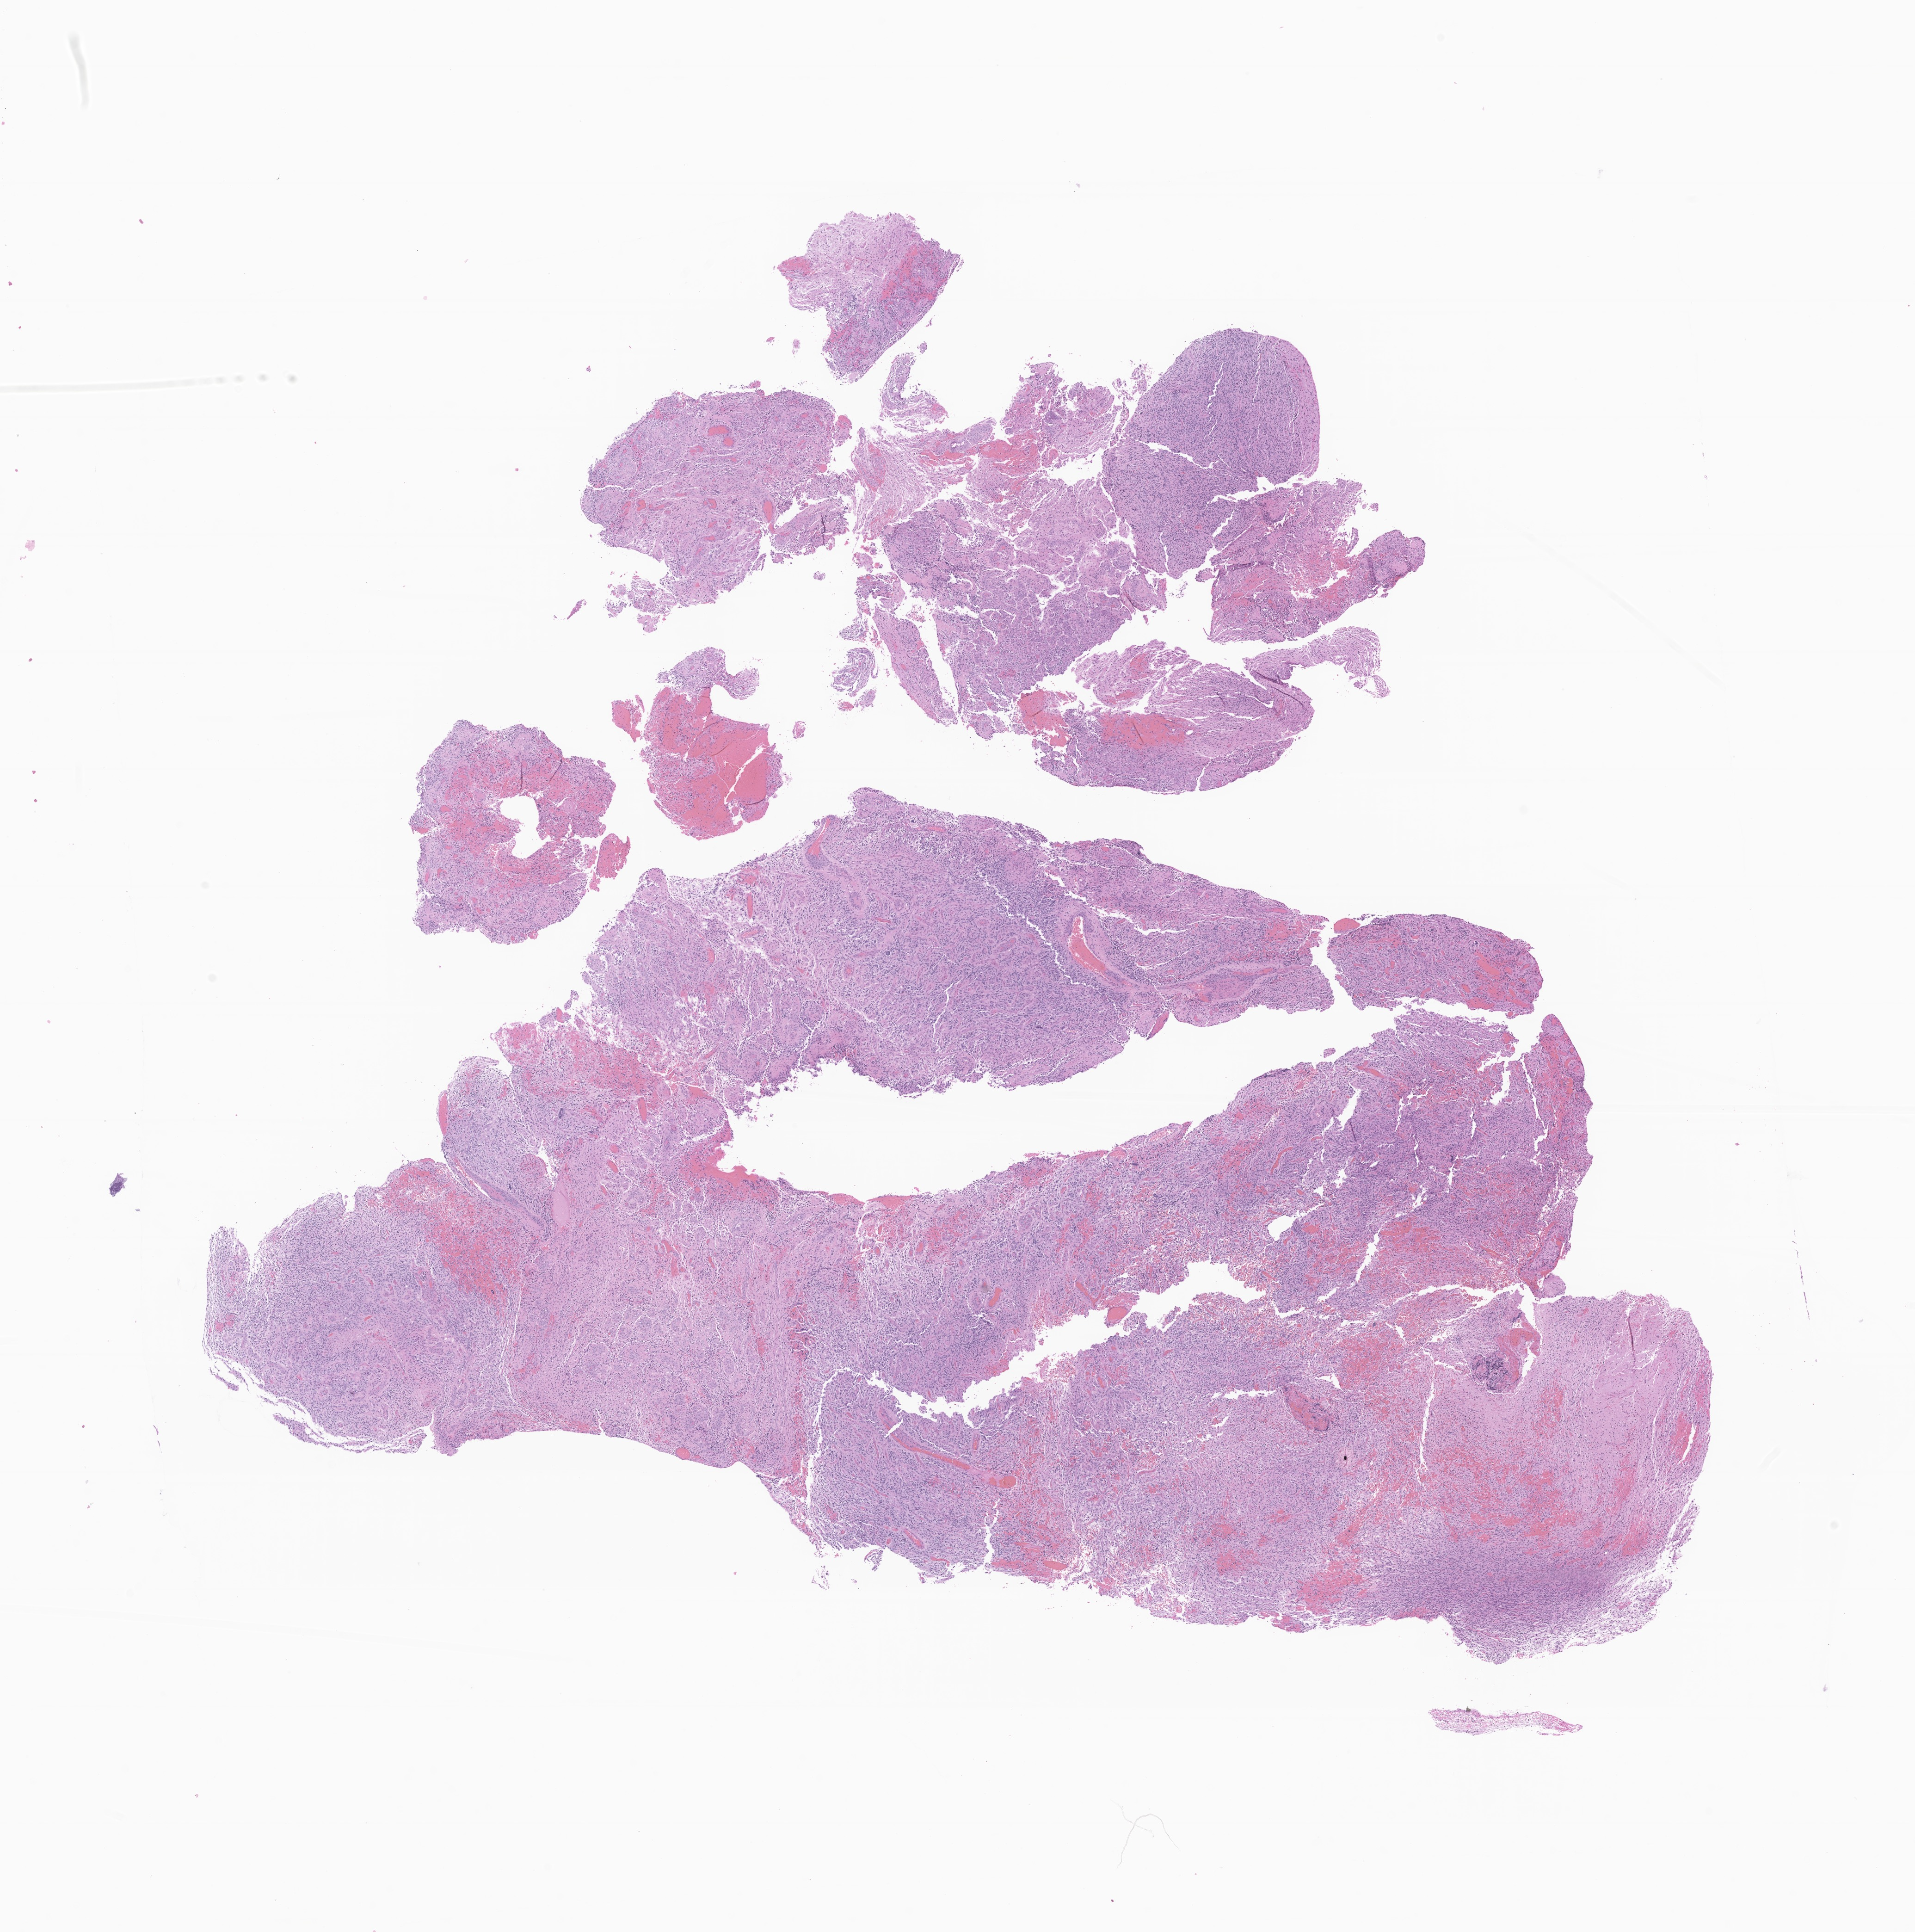
Hematoxylin and eosin (H&E) whole-slide image of tumor tissue from the frontal lobe — whole scanned area (about 17.5 x 17.6 mm) shown as a low-resolution overview, formalin-fixed paraffin-embedded section. Patient male; age 178 months (14 years 10 months).
Diagnosis (ICD-O-3 morphology term): Neoplasm, uncertain whether benign or malignant.